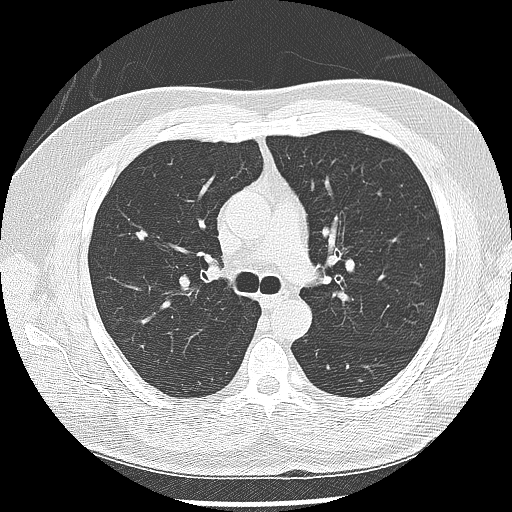
Low-dose screening chest CT, one axial slice; position 175 of 265 along the scan axis; reconstruction kernel LUNG; lung window (W 1500 / L -600 HU); 2.5 mm slice thickness; 512 × 512 image matrix.
Outlined on this slice (expert manual segmentation):
- lesion 1 (tumor, upper lobe of right lung): bounding box [x1, y1, x2, y2] px = [136, 230, 148, 241]